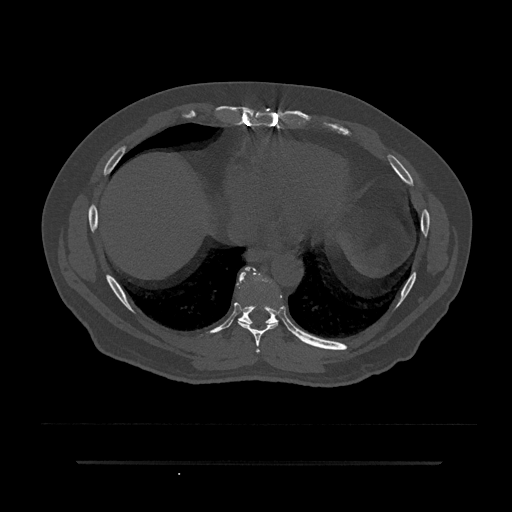
CT including the spine, one axial slice. 120 kVp. Bone window (W 1800 / L 400 HU). 0.5 mm slice thickness. 512 × 512 image matrix, field of view 464 × 464 mm. Patient: male, 59 years. Case-level facts recorded for this patient, not image findings: primary cancer: bile ducts; vertebrae with lytic lesions (as recorded): T10.
Annotated regions visible in this slice (semi-automatic segmentation, software-assisted and operator-edited):
- T7 vertebra: bounding box [x1, y1, x2, y2] px = [256, 349, 260, 353]
- T8 vertebra: [238, 267, 278, 353]
- T9 vertebra: [236, 267, 280, 325]